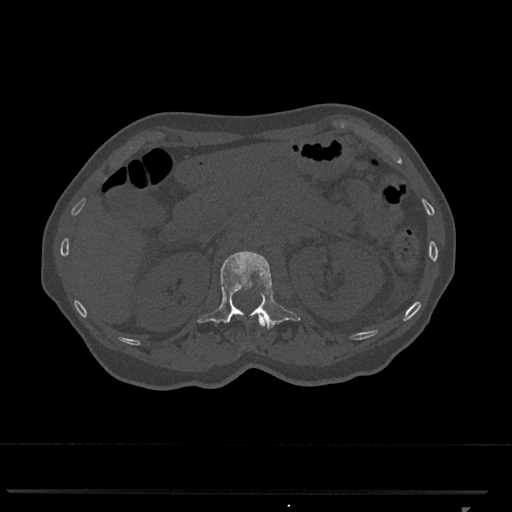
CT including the spine, one axial slice; position 411 of 793 along the scan axis; 120 kVp; bone window (W 1800 / L 400 HU); 512 × 512 image matrix, field of view 380 × 380 mm. Patient: female, 62 years. Case-level facts recorded for this patient, not image findings: primary cancer: renal.
Structures marked on this image (semi-automatically segmented with operator editing):
- L1 vertebra: bounding box [x1, y1, x2, y2] px = [198, 251, 301, 329]
- T12 vertebra: [258, 316, 265, 327]